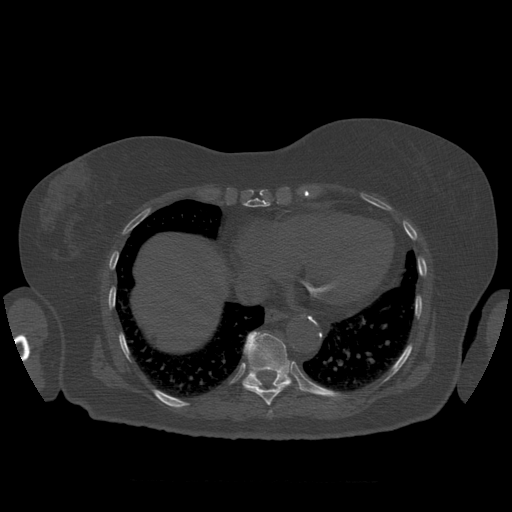
CT including the spine, one axial slice. Position 351 of 399 along the scan axis. Reconstruction kernel STANDARD. 120 kVp. Bone window (W 1800 / L 400 HU). 512 × 512 image matrix, field of view 404 × 404 mm. Patient age 81 years. Case-level facts recorded for this patient, not image findings: primary cancer: renal; vertebrae with lytic lesions (as recorded): L1.
Outlined on this slice (semi-automatically segmented with operator editing):
- T10 vertebra: bounding box <244,332,301,391> (left, top, right, bottom; pixels)
- T8 vertebra: <270,411,272,413>
- T9 vertebra: <243,350,286,406>